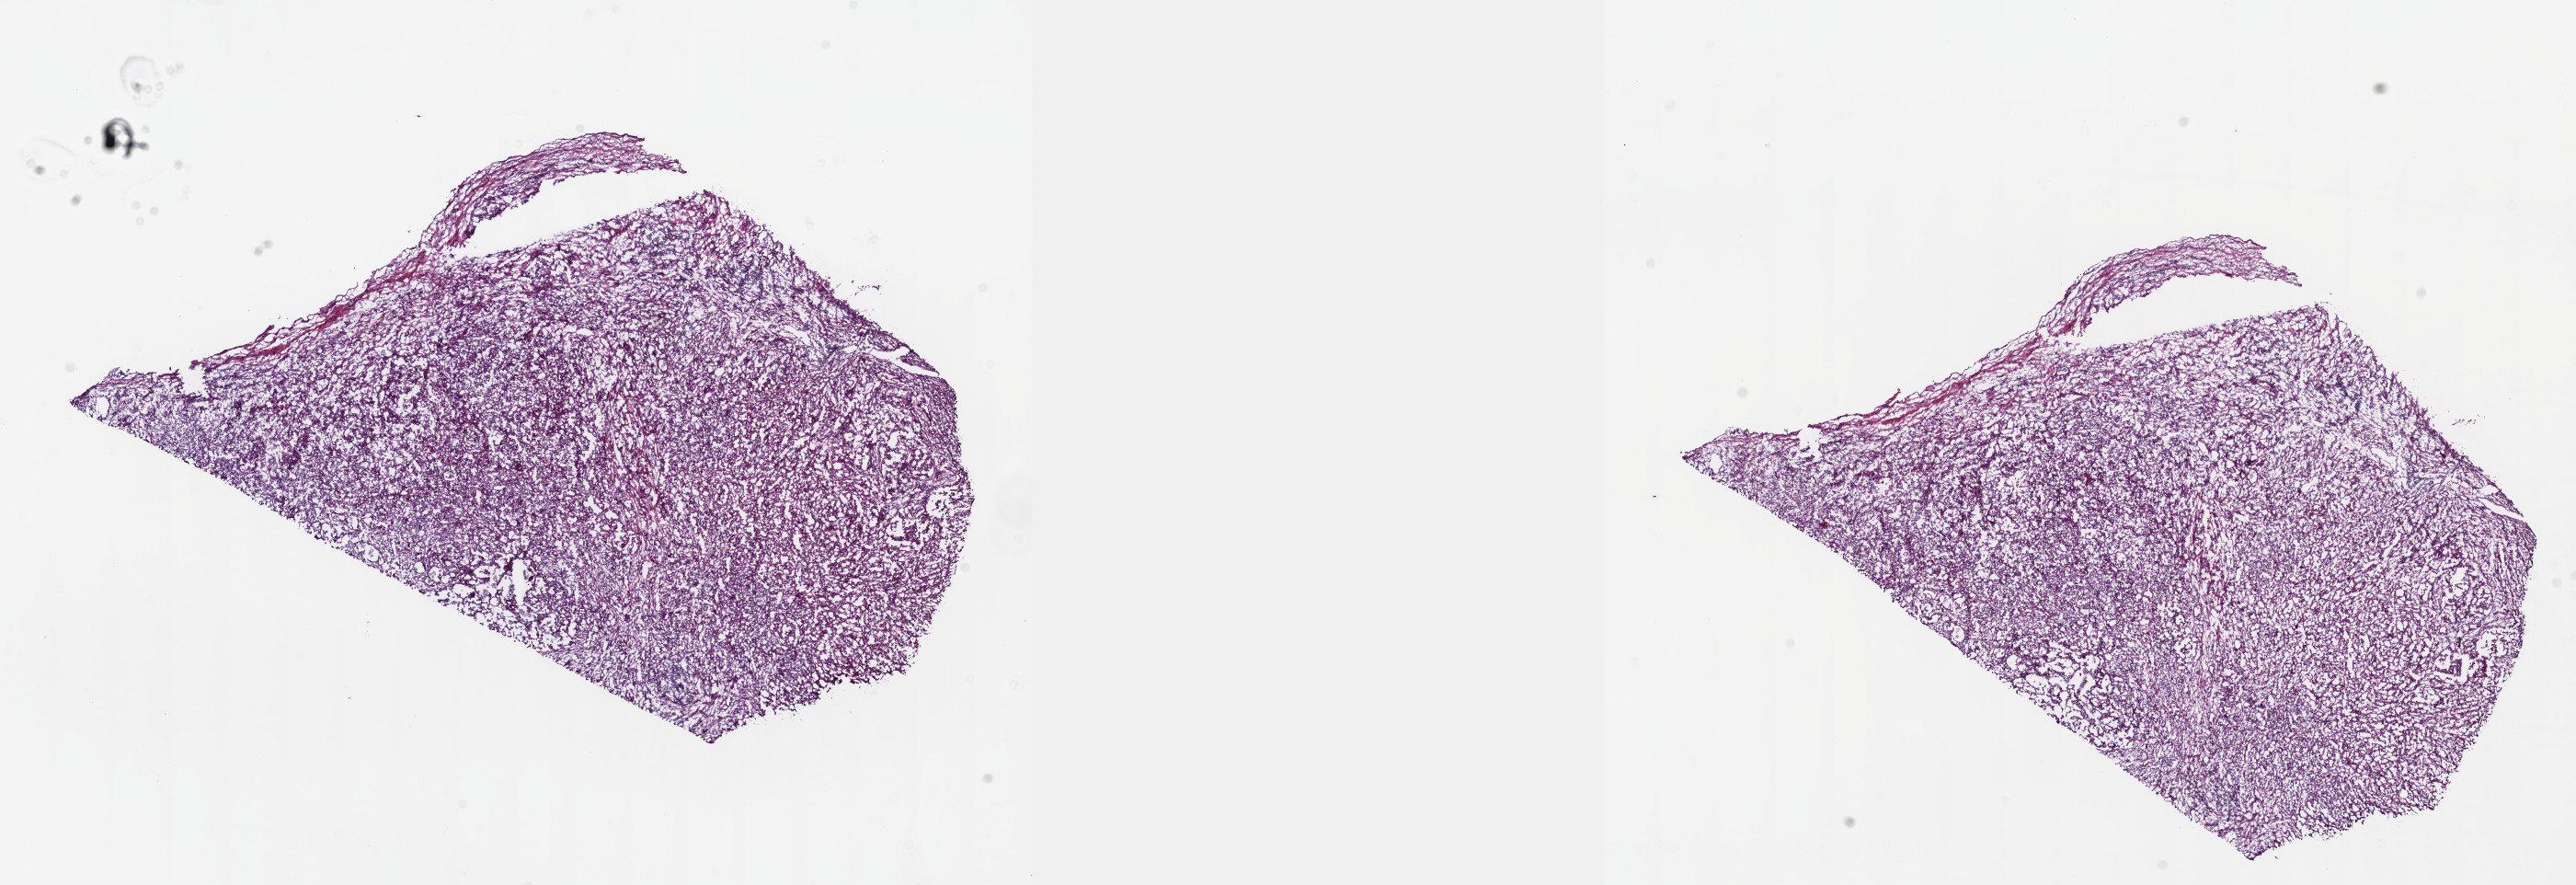
Whole-slide histology image, H&E-stained — a low-resolution overview of the entire scanned area, about 22.6 x 7.8 mm (from a 40x scan), frozen section, sample: primary tumour, mesothelium. Female patient; age at initial diagnosis 71 years. Pathologist review of this section (percent, as recorded): tumour cells 100%, tumour nuclei 75%, normal cells 0%, stromal cells 0%, necrosis 0%. Inflammatory infiltration, as recorded: lymphocyte infiltration 2%, monocyte infiltration 0%, neutrophil infiltration 0%.
AJCC pathologic stage: III. Histologic diagnosis: Epithelioid mesothelioma, malignant. Laterality: right. TNM: T2 N2 M0.